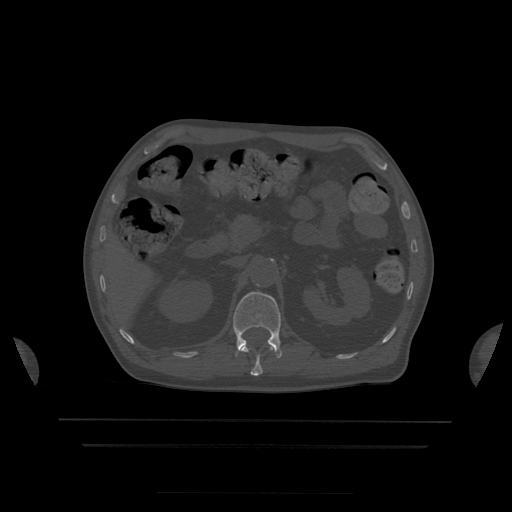
CT including the spine, one axial slice. Slice 180 of 522 in the series (ordered by position). Bone window (W 1800 / L 400 HU). 1.25 mm slice thickness. 512 × 512 image matrix. Patient age 68 years. From the clinical record (not read from this slice): primary cancer: urothelial.
Outlined on this slice (semi-automatically segmented with operator editing):
- L1 vertebra: bounding box <233,292,283,358> (left, top, right, bottom; pixels)
- T12 vertebra: <241,346,273,376>